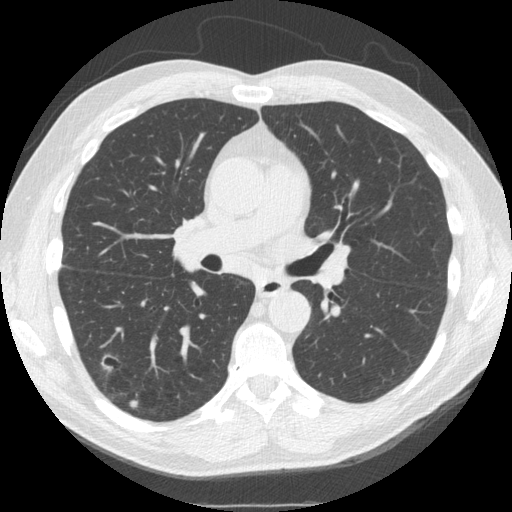
Low-dose screening chest CT, one axial slice. Slice 92 of 162 in the series (ordered by position). 120 kVp. Lung window (W 1500 / L -600 HU). 512 × 512 image matrix, field of view 360 × 360 mm.
Annotated regions visible in this slice (outlined manually by an expert reader):
- lesion 1 (nodule, lower lobe of right lung): bounding box <101,354,116,371> (left, top, right, bottom; pixels)
- lesion 2 (tumor, lower lobe of right lung): <130,399,139,408>